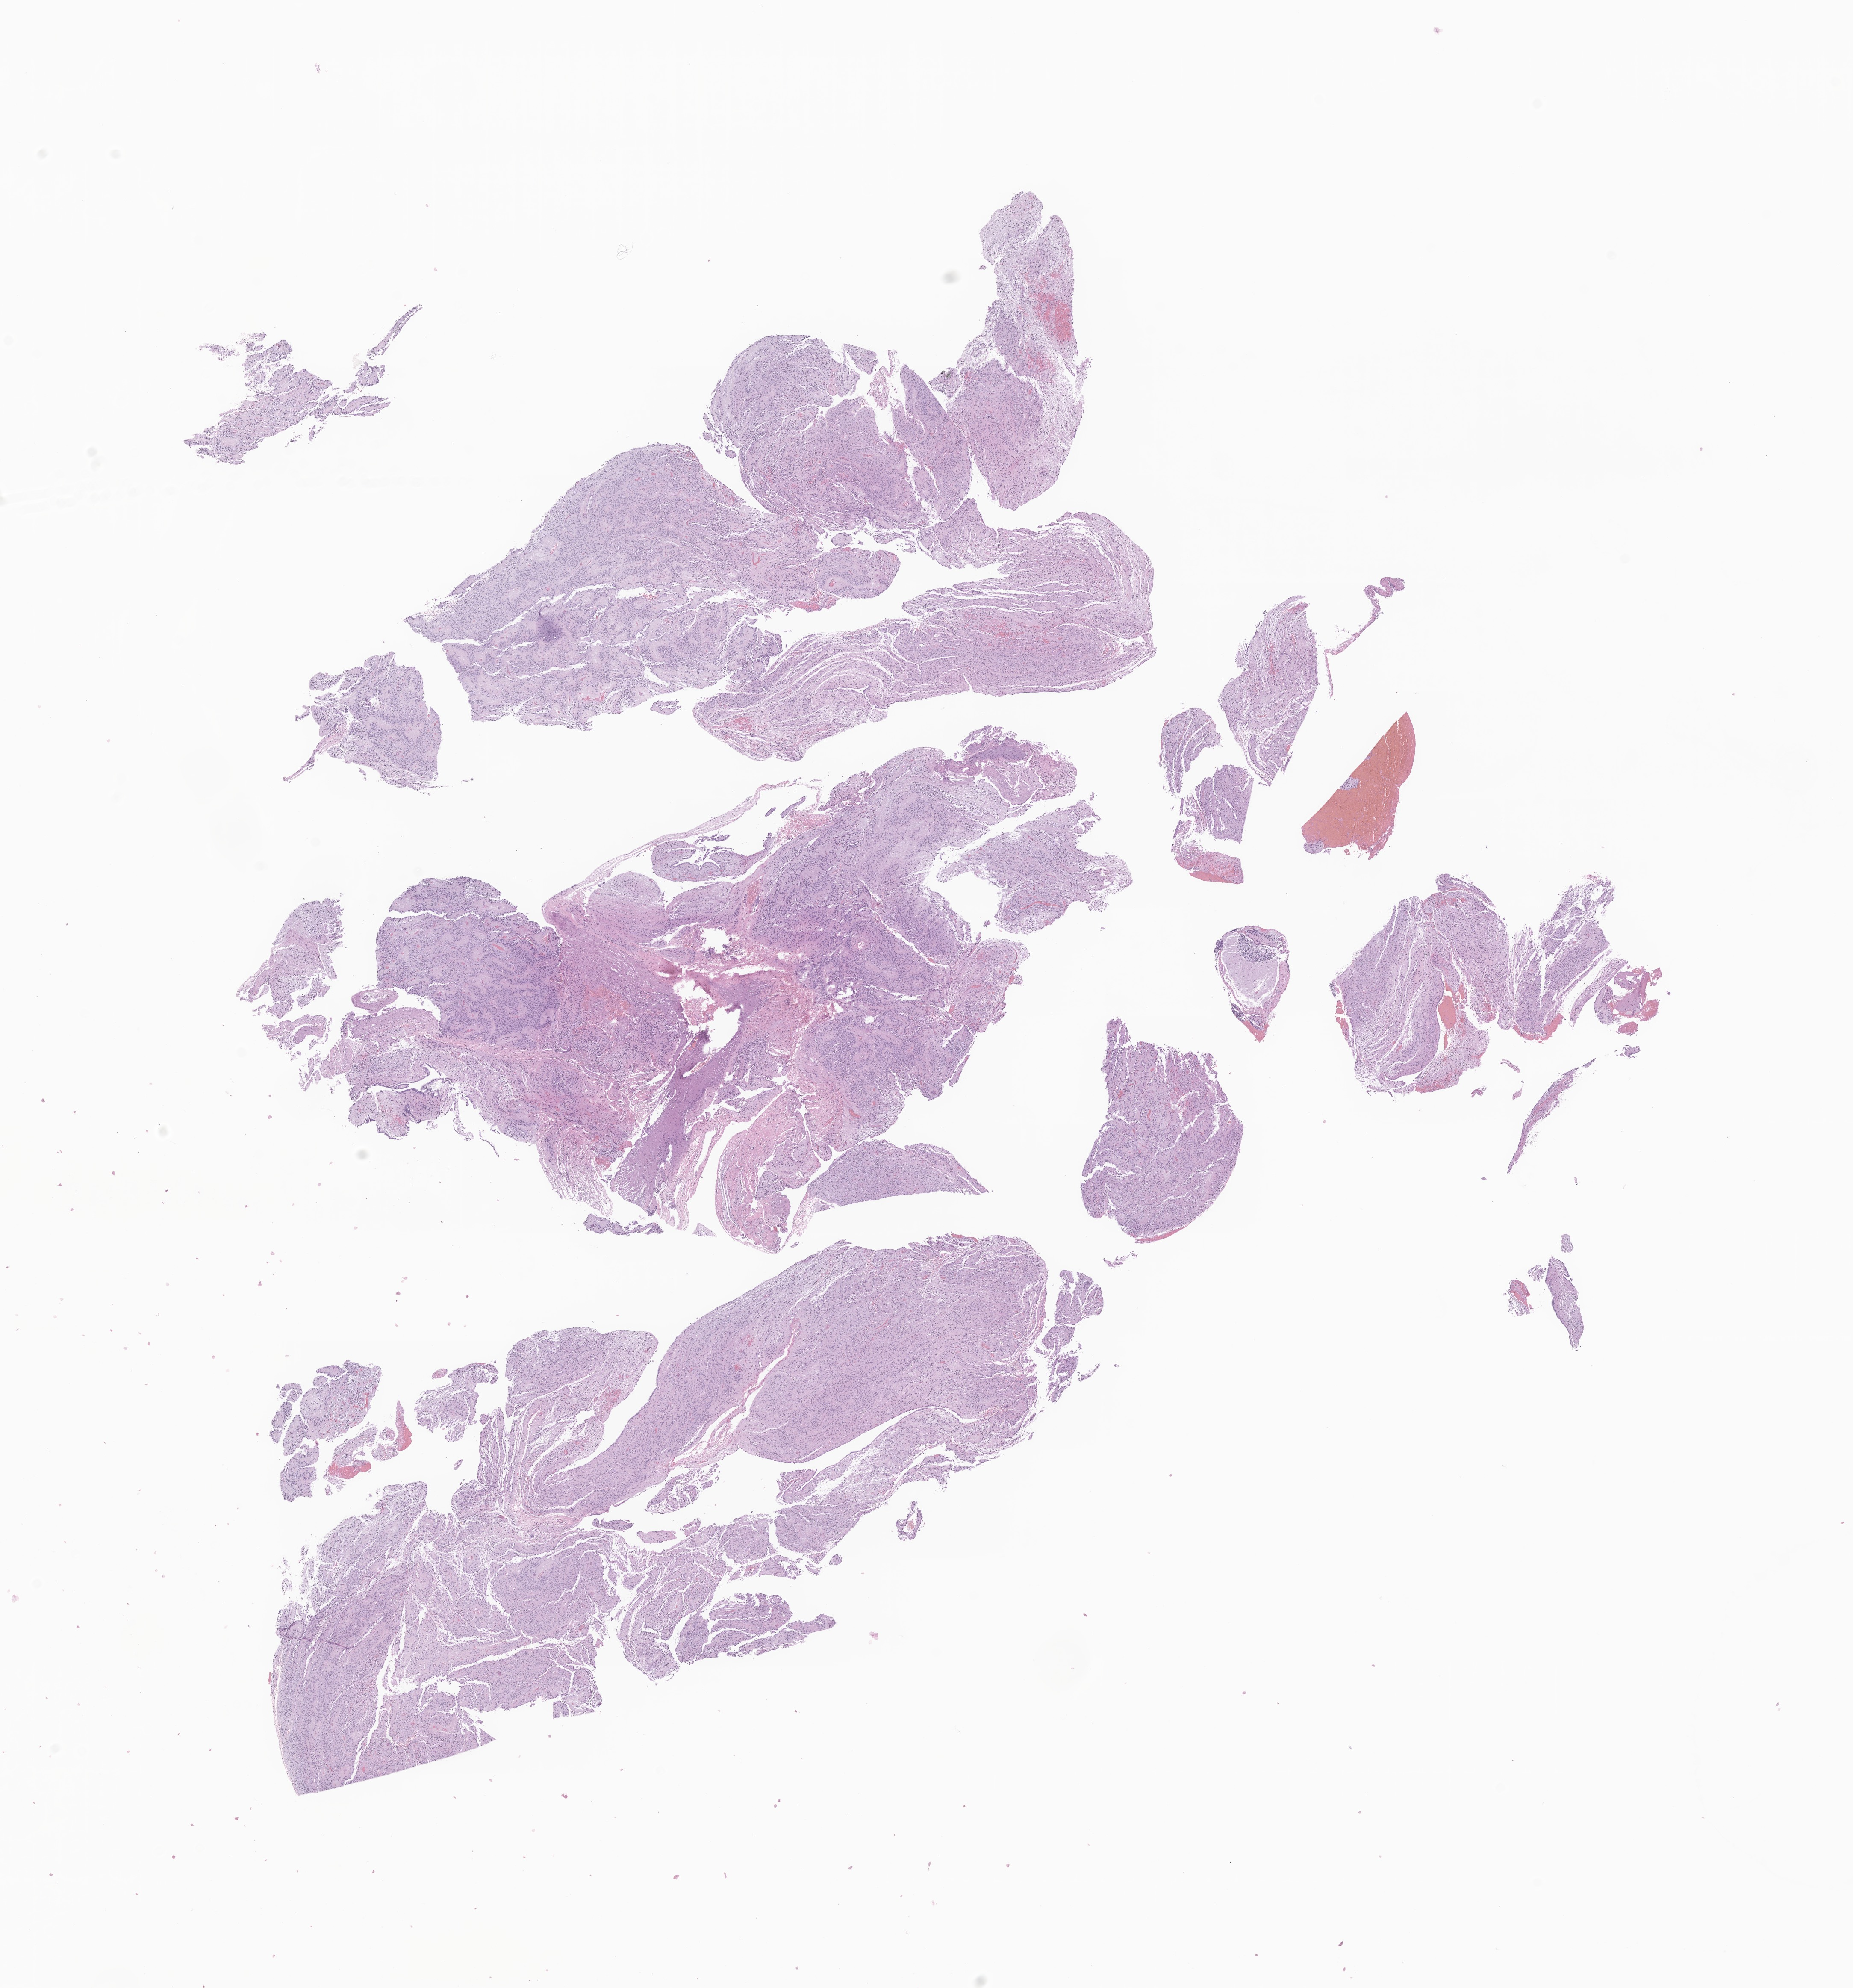
H&E whole-slide image of tumor tissue from the brain, low-resolution overview of the scanned area, about 18.3 x 19.6 mm, FFPE section. Patient female; age 762 days (about 2.1 years).
Diagnosis (ICD-O-3 morphology term): Ependymoma, NOS.